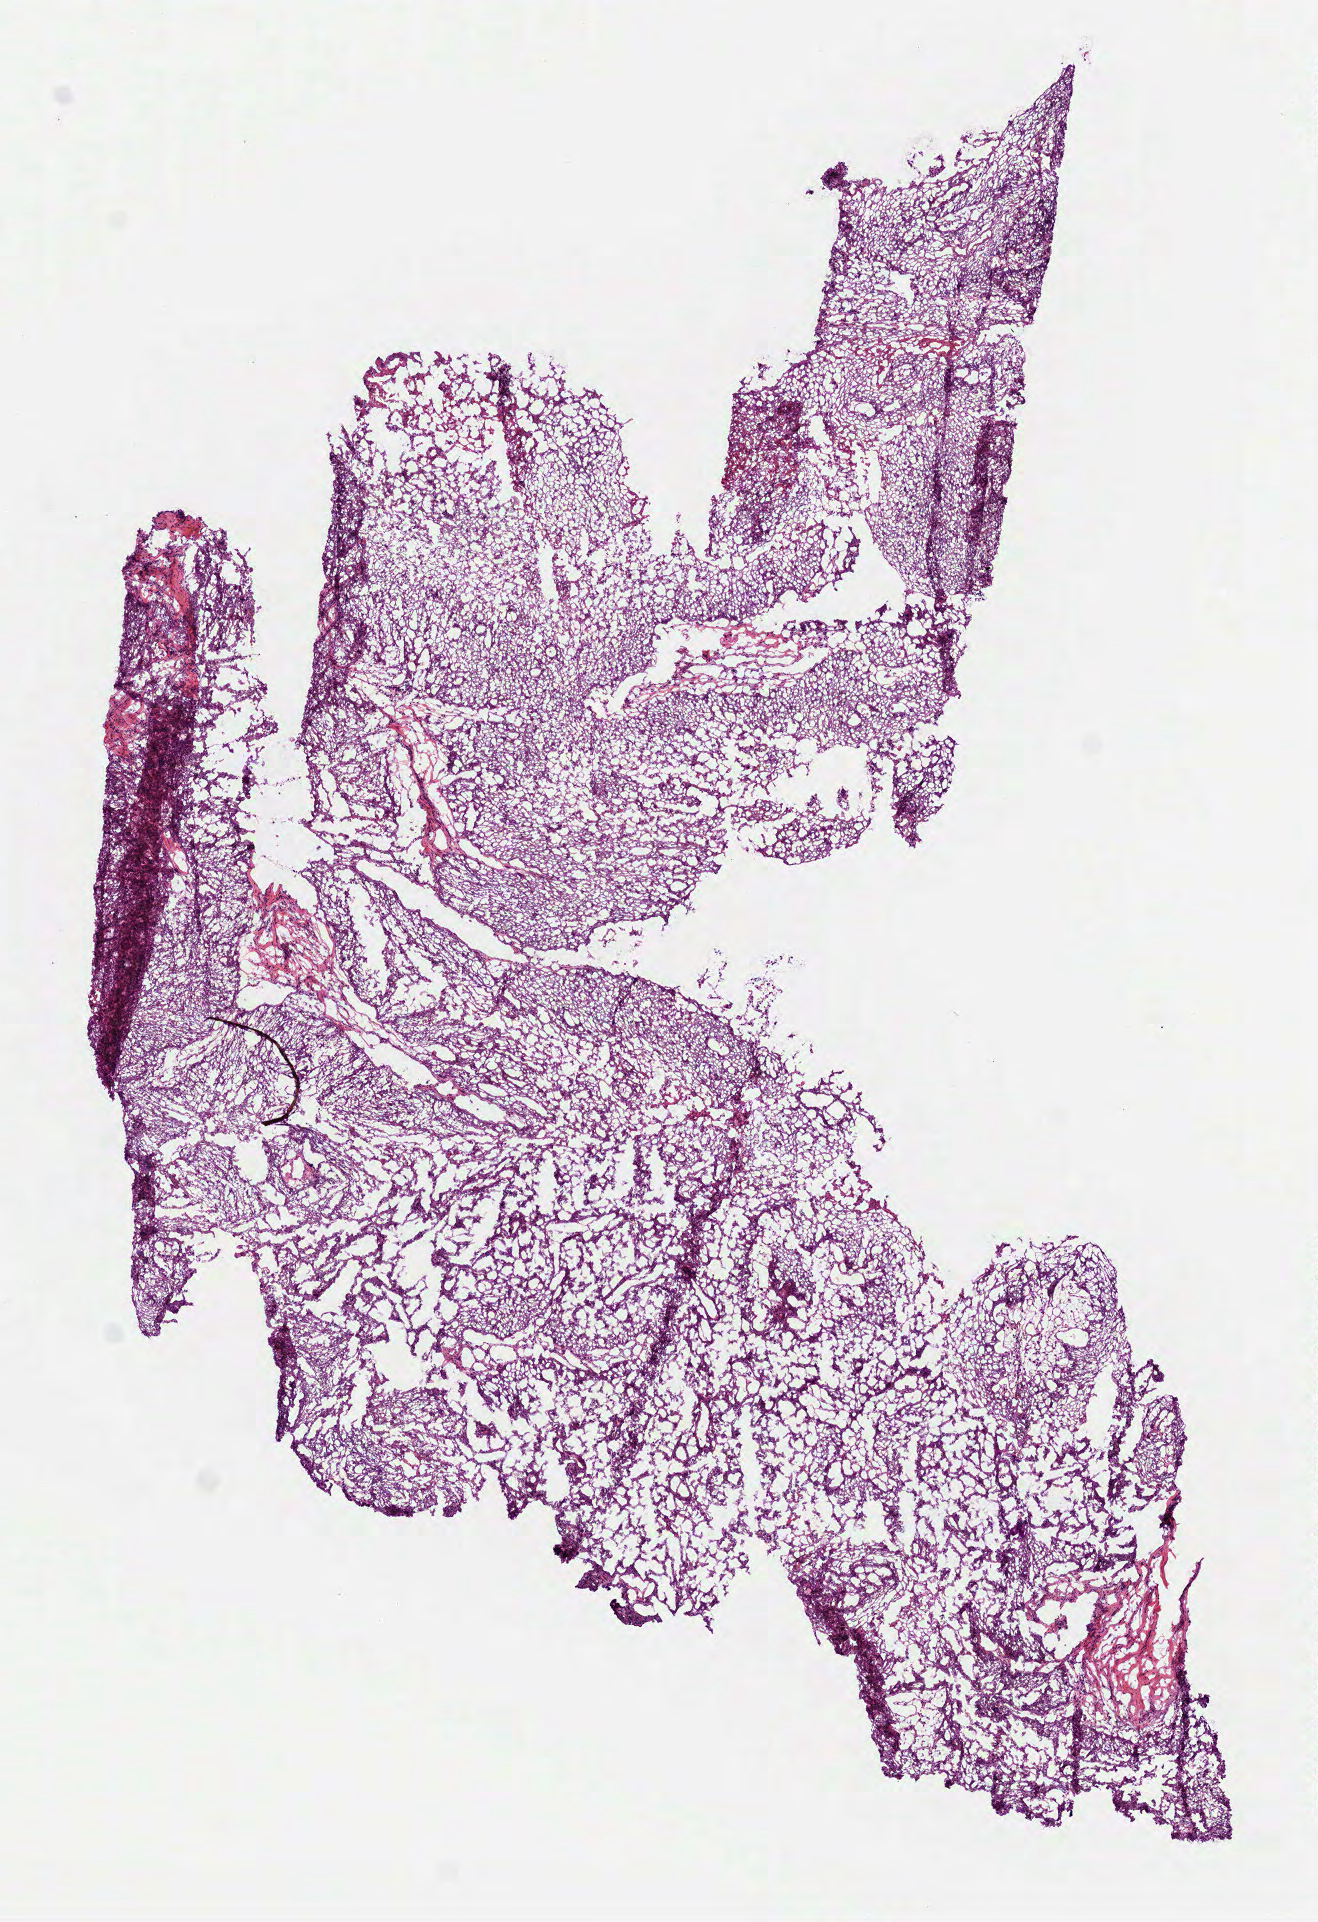
Digitized H&E tissue section (whole slide) — whole scanned area (about 5.3 x 7.8 mm) shown as a low-resolution overview, frozen section, primary tumour sample from the head and neck. Male, age 64 years at initial diagnosis. Histologic grade: G1 (well differentiated). Composition of this section per pathologist review: tumour cells 90%, tumour nuclei 80%, normal cells 0%, stromal cells 10%, necrosis 0%.
- AJCC pathologic stage: IVA
- diagnosis: Squamous cell carcinoma, NOS (larynx, NOS)